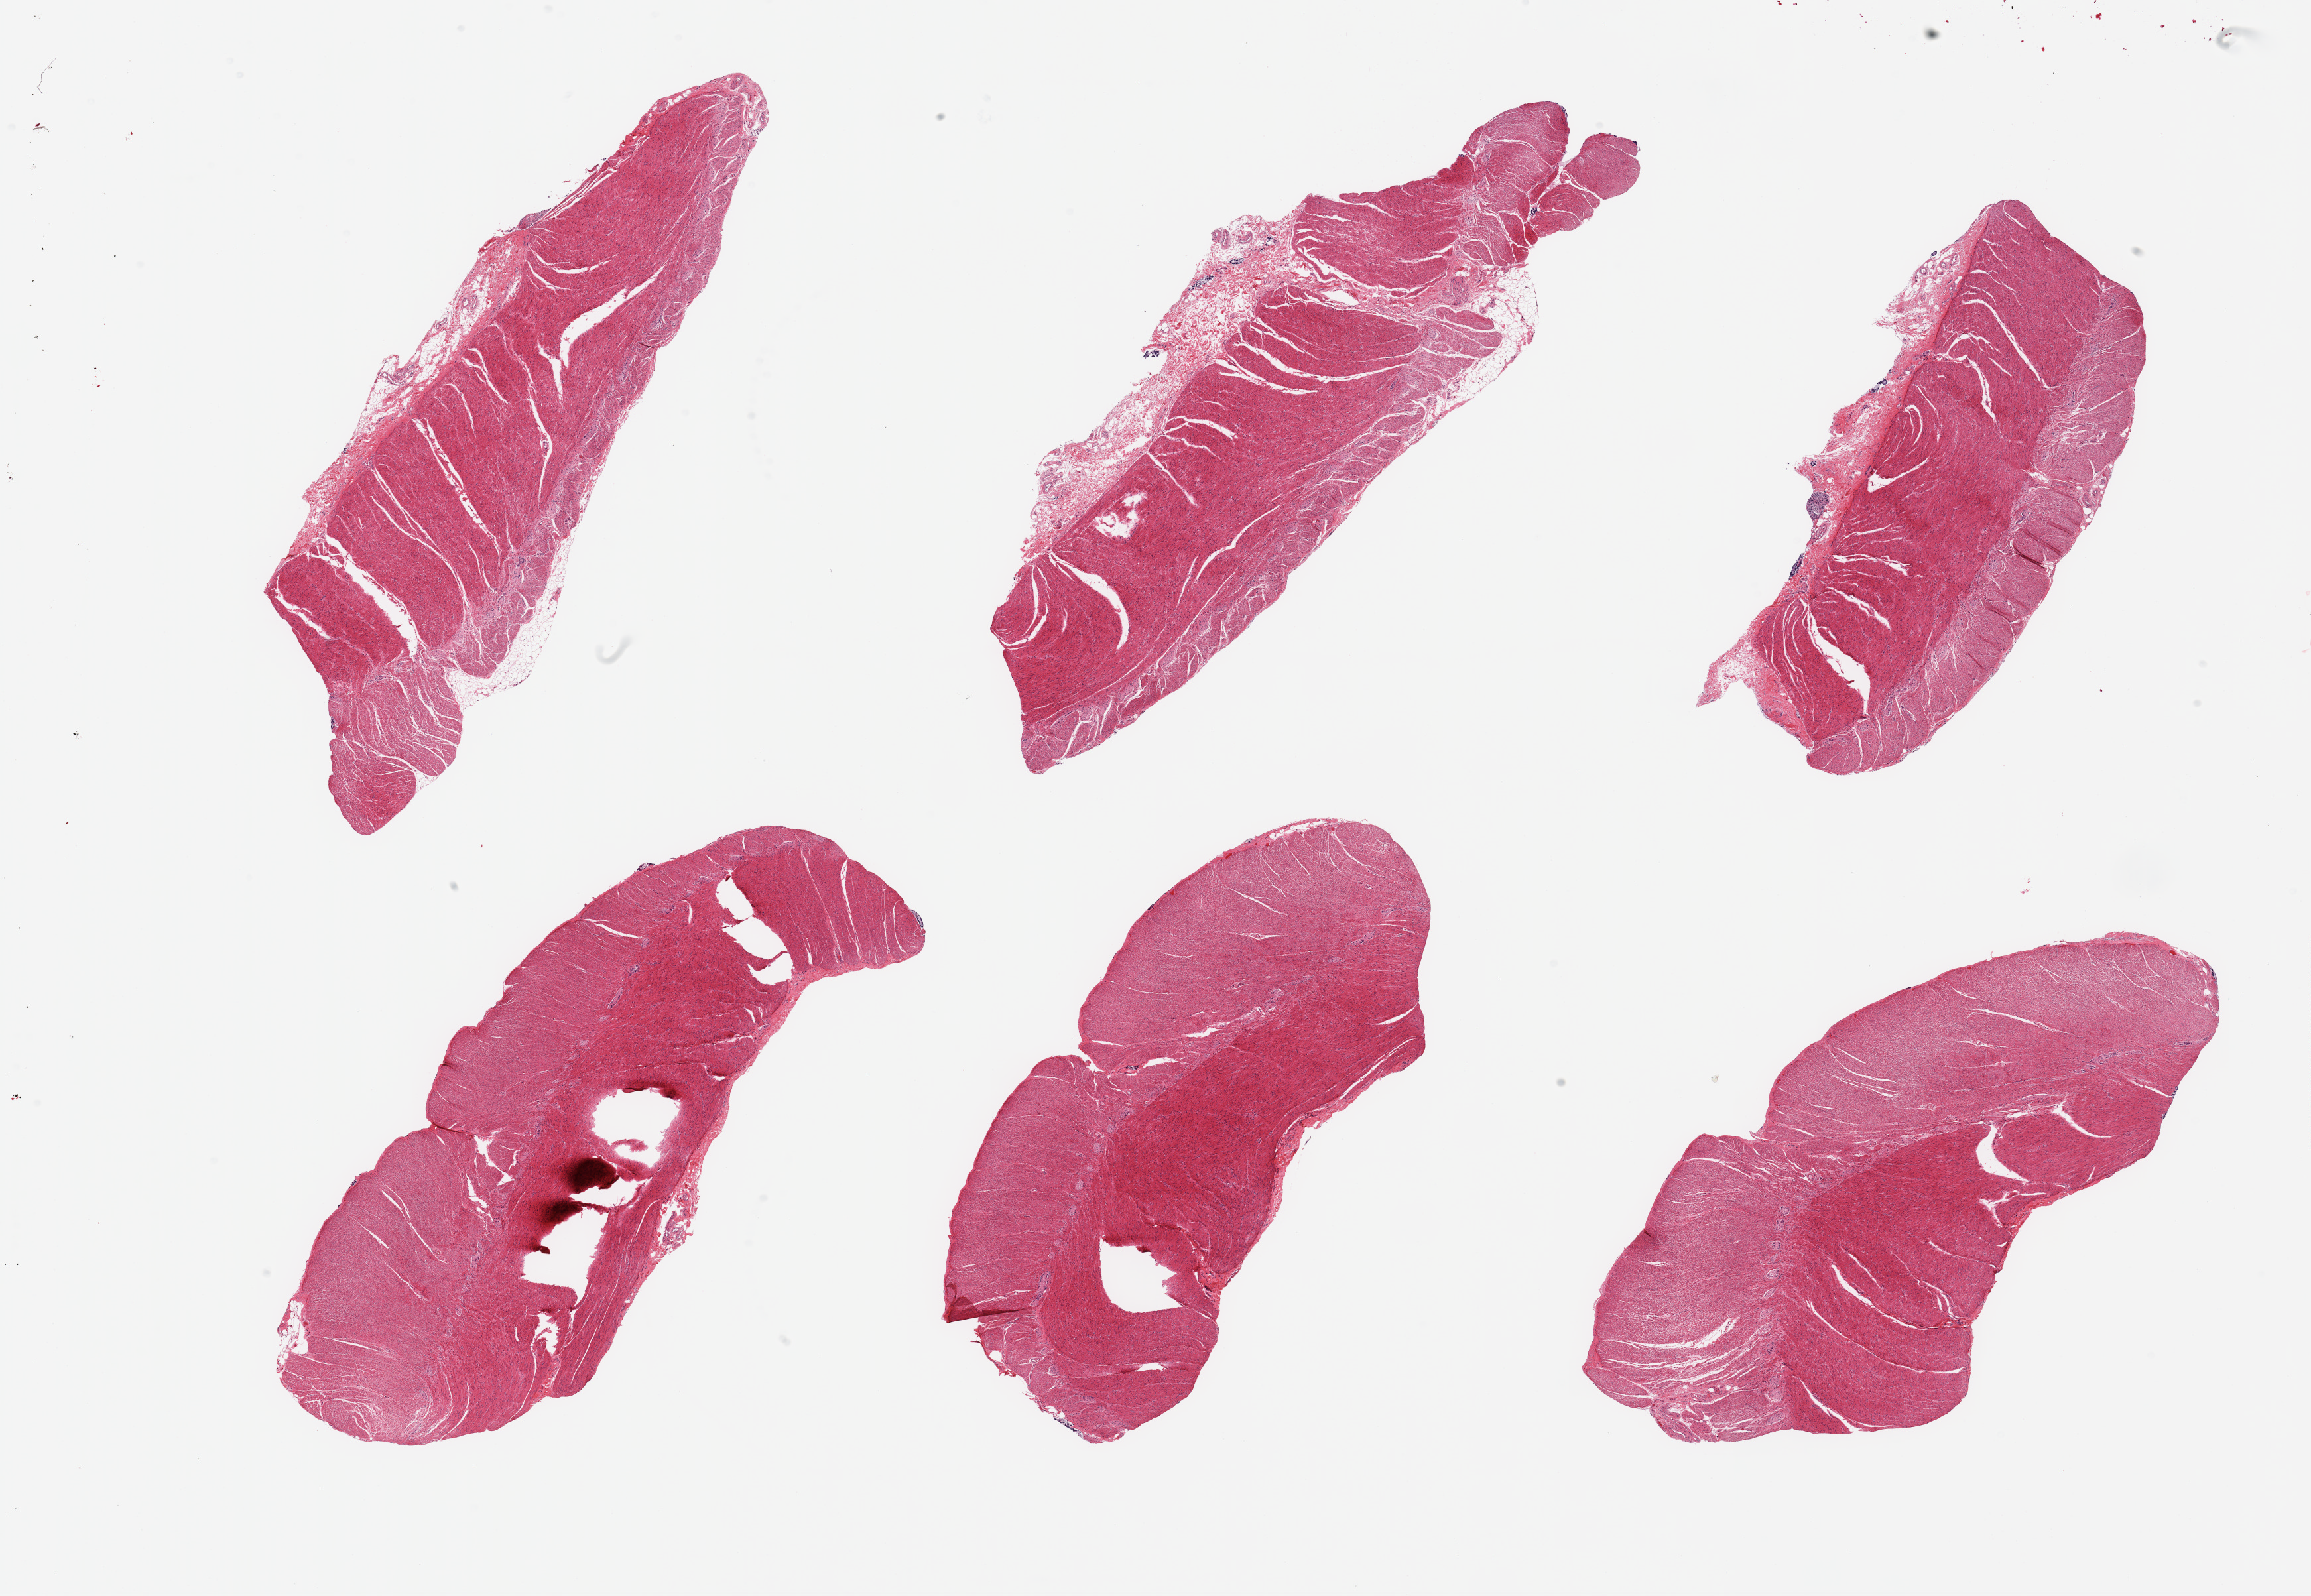
Digitized H&E-stained section, brightfield — whole scanned area (about 27.6 x 19.0 mm) shown as a low-resolution overview. PAXgene-fixed, paraffin-embedded tissue. Sampled site (target tissue): sigmoid colon. Donor tissue sample. Donor: male.
- review note (as recorded): 6 pieces; target muscularis with scant detached fragments of colonic glands in association with a few pieces